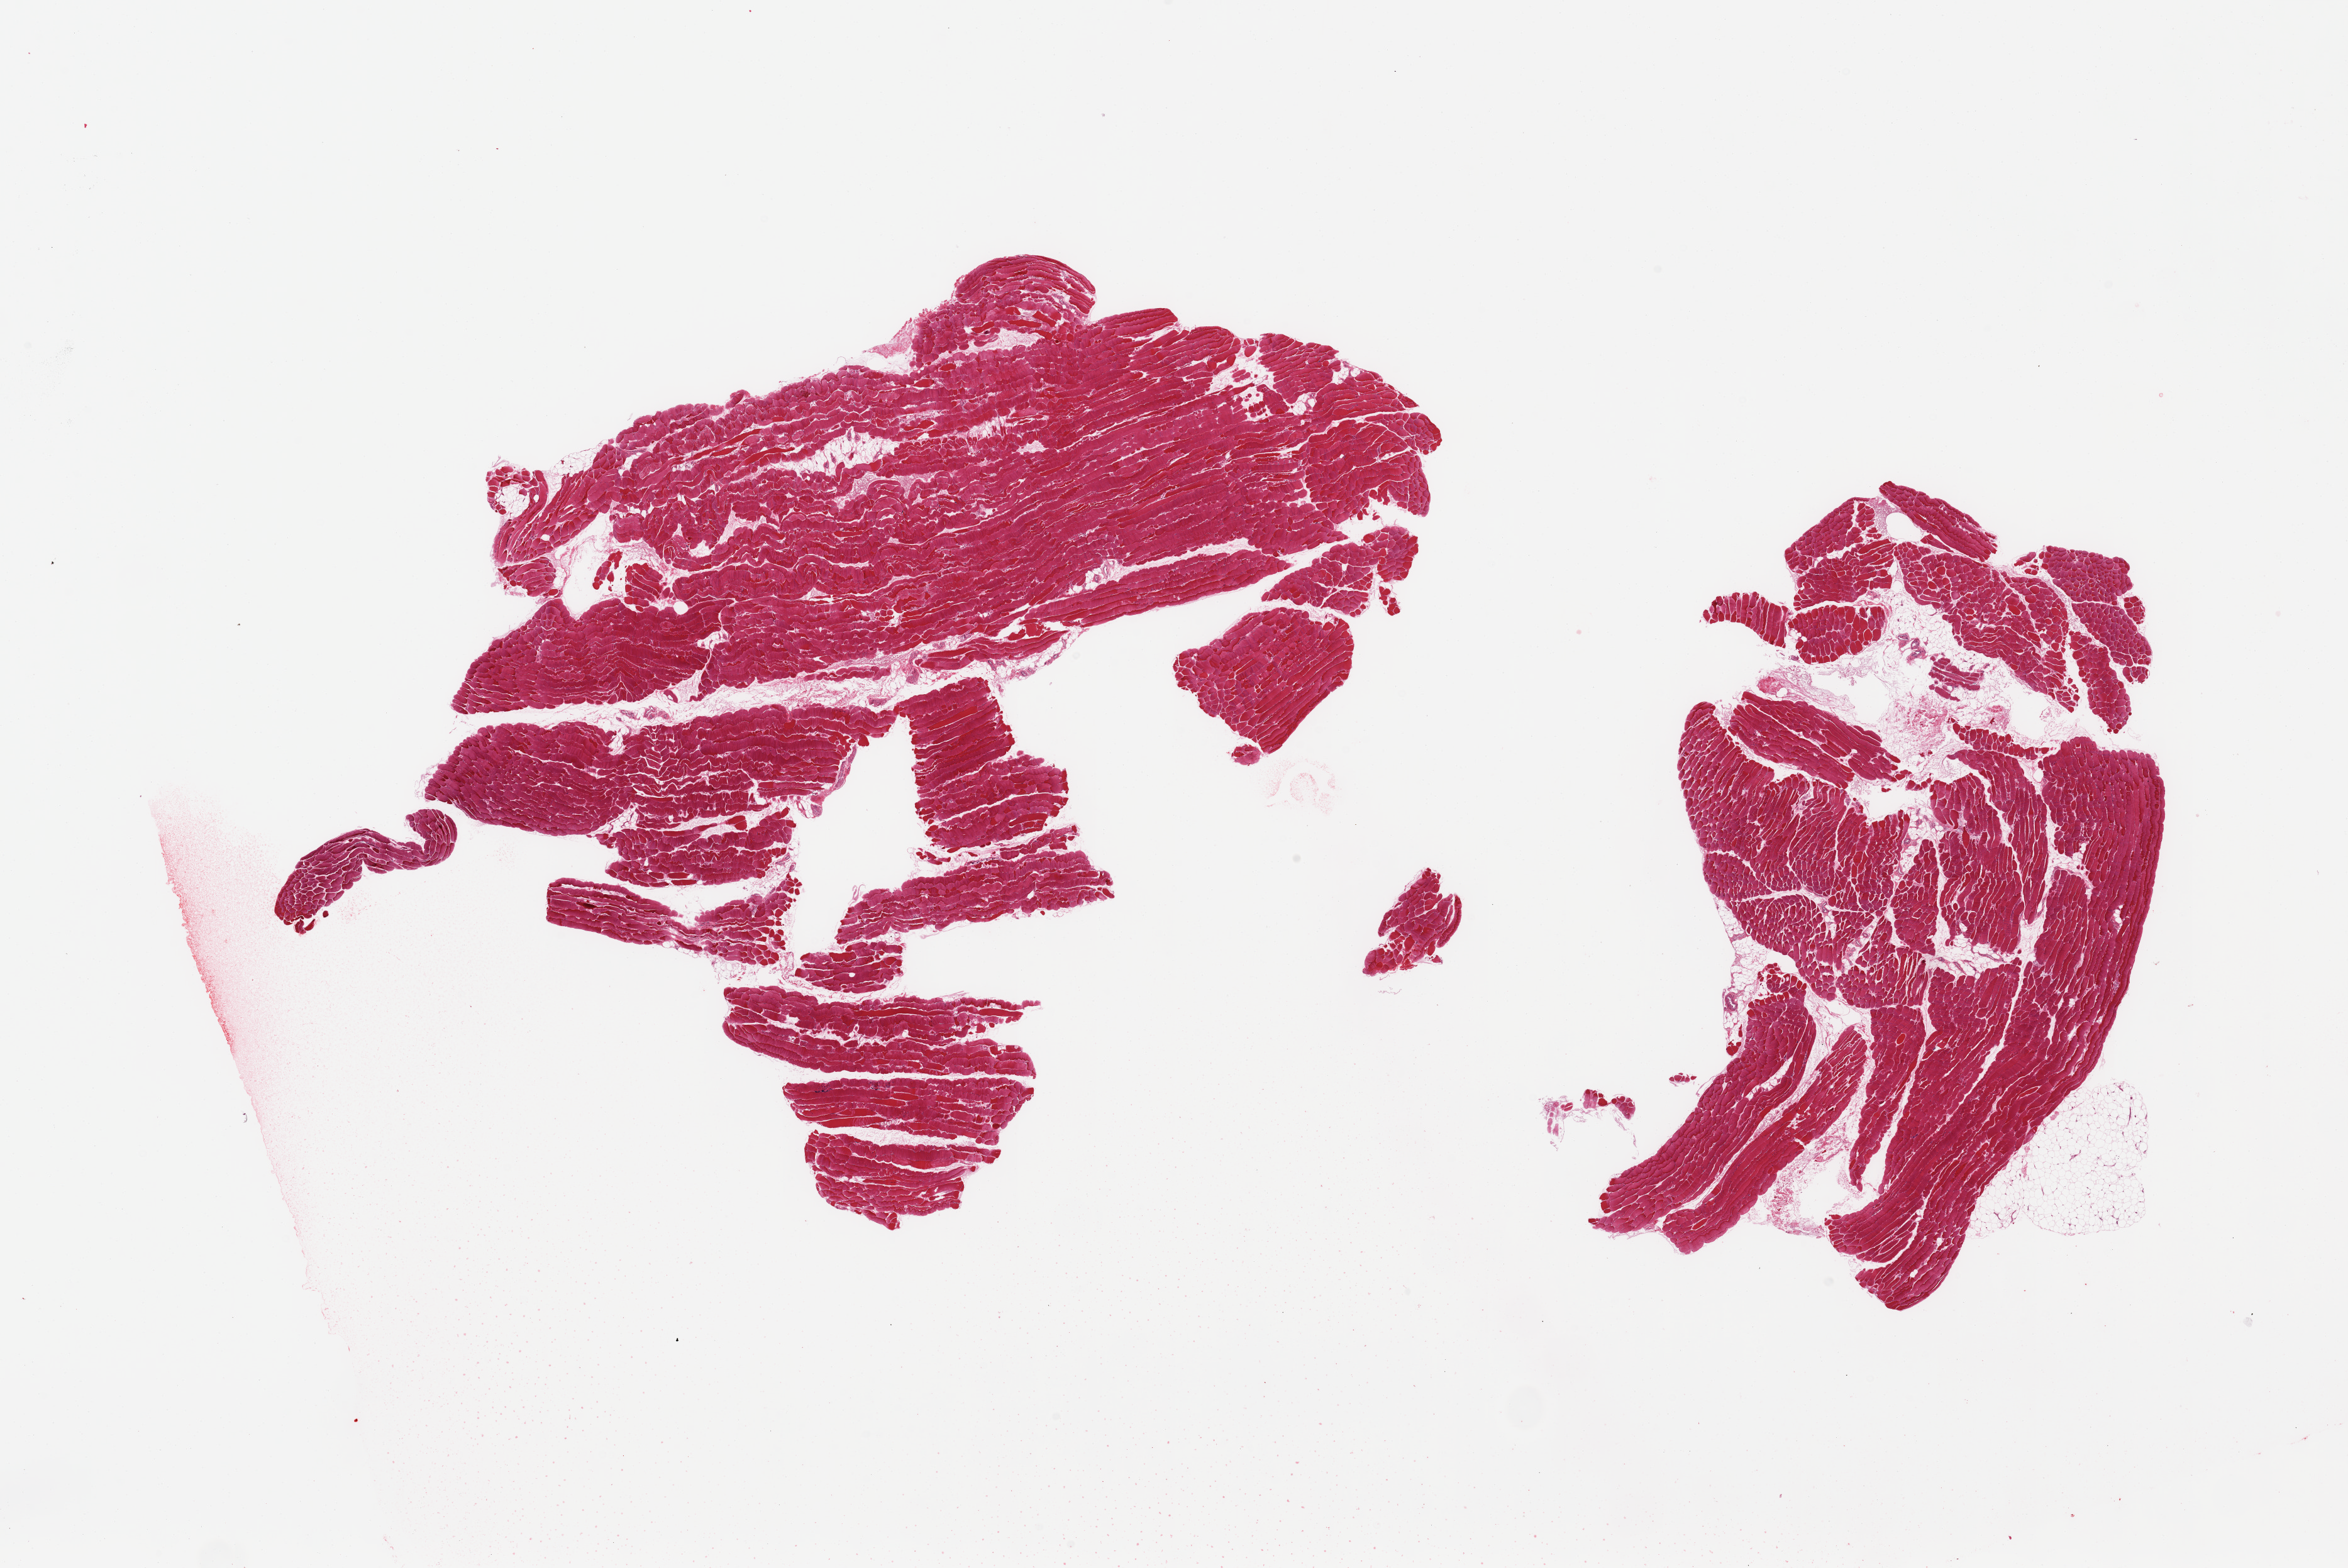
Digitized hematoxylin and eosin (H&E)-stained section — low-resolution overview of the scanned area, about 29.5 x 19.7 mm; PAXgene-fixed paraffin-embedded (PFPE) section; section of skeletal muscle (target tissue); donor tissue sample. Donor sex: female.
* review note (as recorded): 2 pieces, ~10% interstital fat/vascular elements